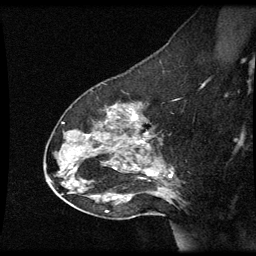
Breast MRI (dynamic contrast-enhanced), one sagittal slice. Position 39 of 60 along the scan axis. Dynamic contrast-enhanced series, image 2 of 3 at this slice position (ordered by acquisition). 1.5 T. TE 4.2 ms, TR 8.9 ms. 2 mm slice thickness. 256 × 256 image matrix, field of view 200 × 200 mm. Female patient, age 49 years. Case-level facts recorded for this patient, not image findings: setting: breast cancer imaged before/during neoadjuvant chemotherapy; receptor status: HR-positive, HER2-negative.
Structures marked on this image (semi-automatically segmented with operator editing):
- analysis volume of interest (the breast-tissue region the enhancement analysis was run in; not a lesion): bounding box (x1, y1, x2, y2) in pixels: (46, 92, 177, 205)
- tumour enhancement mask (voxels above the 70 % enhancement threshold inside the analysis volume of interest): (132, 114, 172, 177)